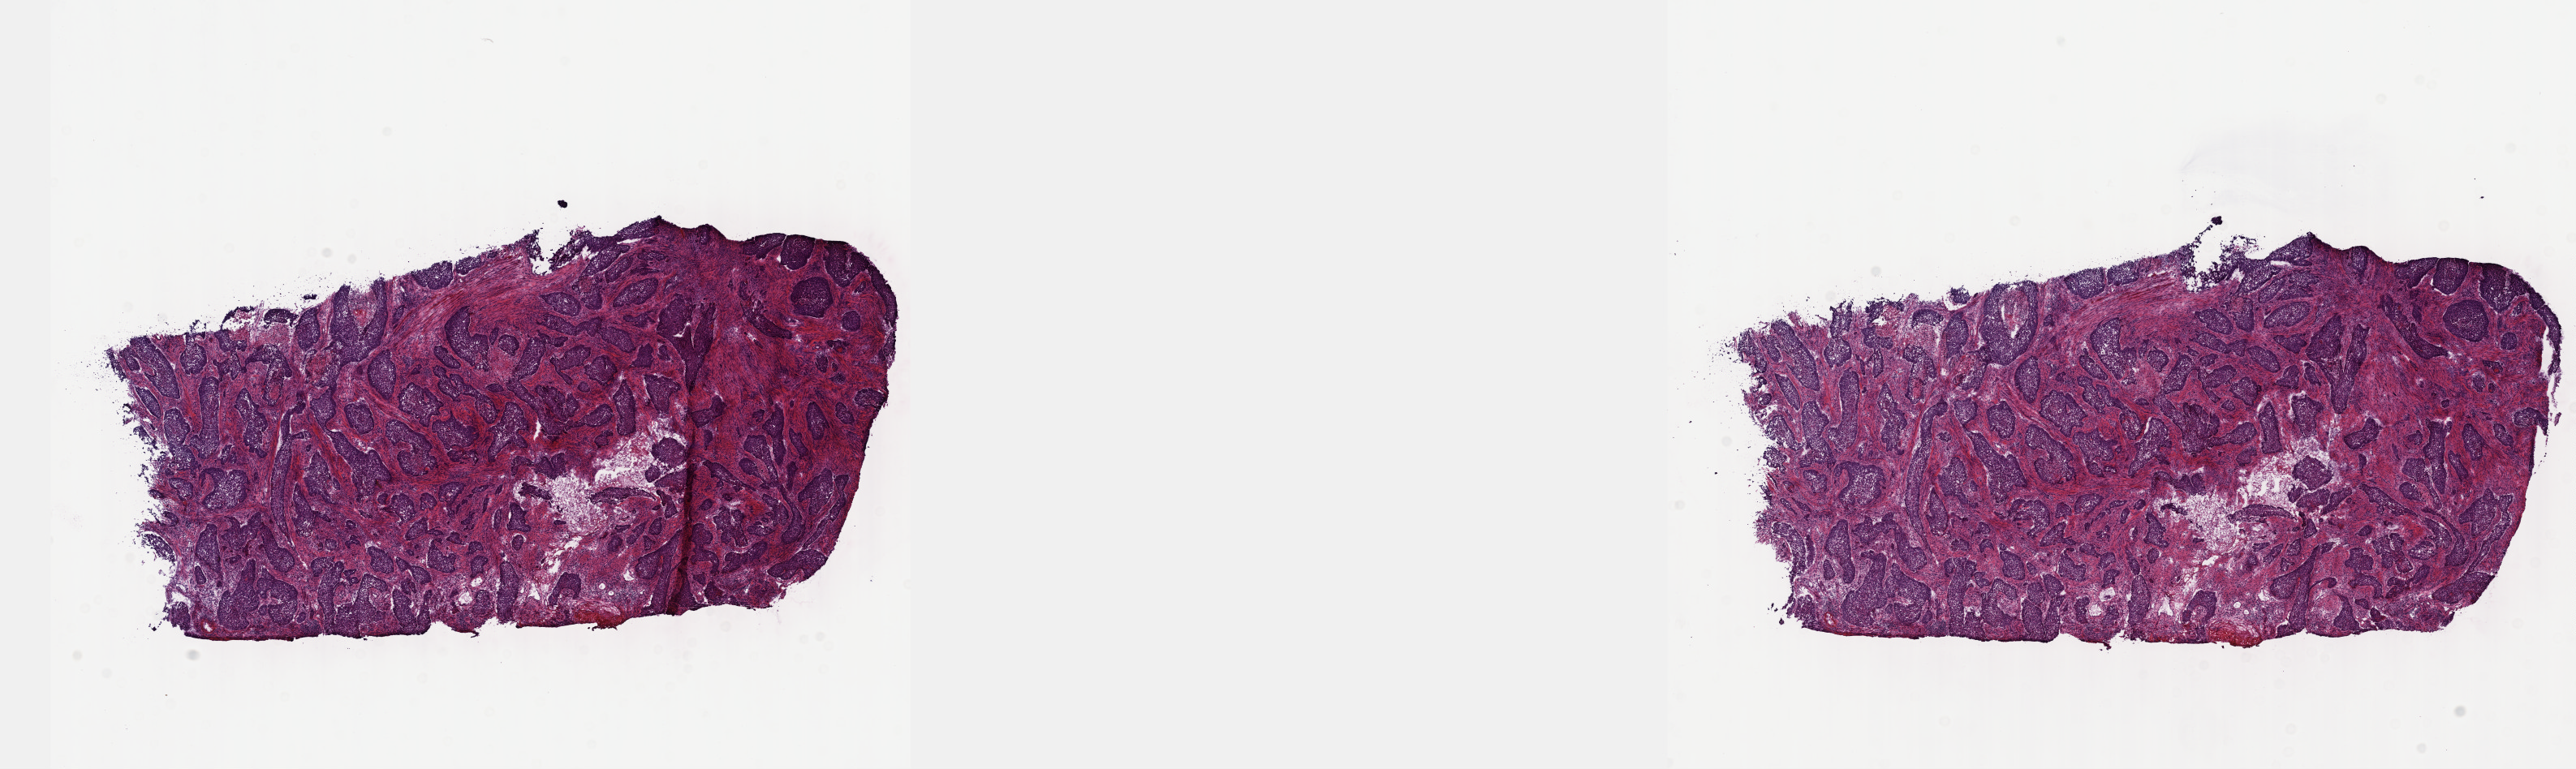
Digitized Hematoxylin and eosin (H&E) stained tissue section (whole slide), low-resolution overview of the scanned area, about 25.7 x 7.7 mm (slide scanned at 40x), frozen section from the top of the tissue portion, sample: primary tumour, head and neck. Male patient; age at initial diagnosis 50 years. Histologic grade: G2 (moderately differentiated). Pathologist review of this section (percent, as recorded): tumour cells 60%, tumour nuclei 60%, normal cells 0%, stromal cells 30%, necrosis 10%. Inflammatory infiltration, as recorded: lymphocyte infiltration 40%, monocyte infiltration 20%, neutrophil infiltration 20%.
* AJCC pathologic stage: IVB
* diagnosis: Squamous cell carcinoma, keratinizing, NOS (oropharynx, NOS)